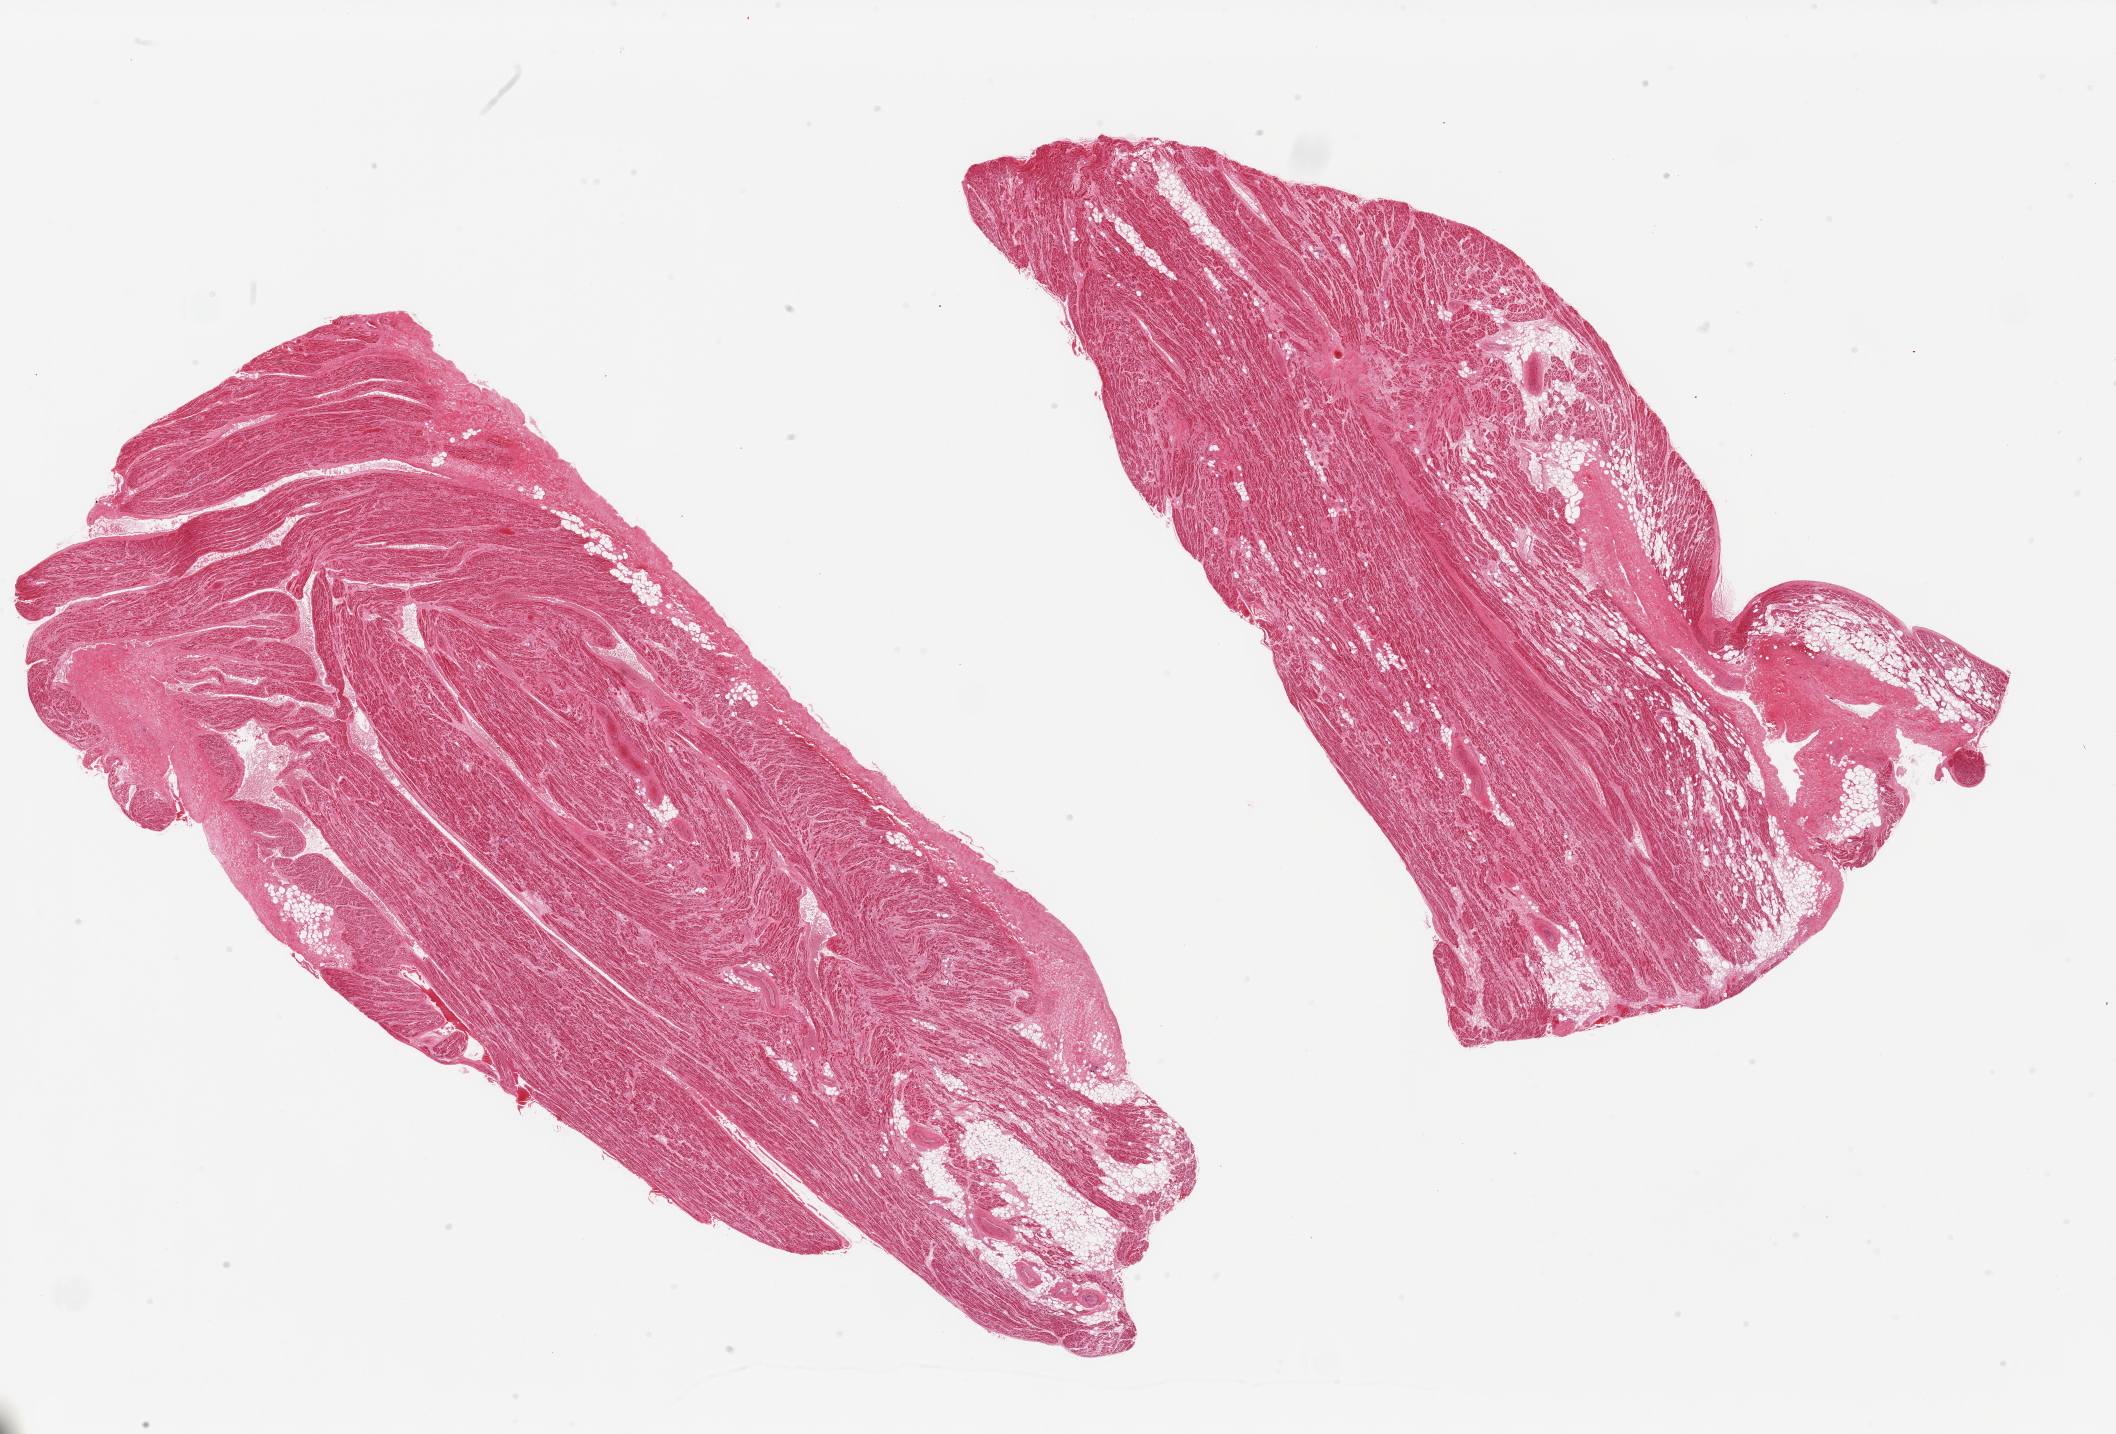
Haematoxylin and eosin whole-slide image, brightfield — a low-resolution overview of the entire scanned area, about 33.5 x 22.7 mm (acquisition: 20x scan); PAXgene-fixed, paraffin-embedded tissue; sampled site (target tissue): auricular appendage; donor tissue sample.
Reviewer comment on this tissue sample: 2 pieces; 10-20% is fibrous/fatty, interstitial and focal patchy fibrosis.